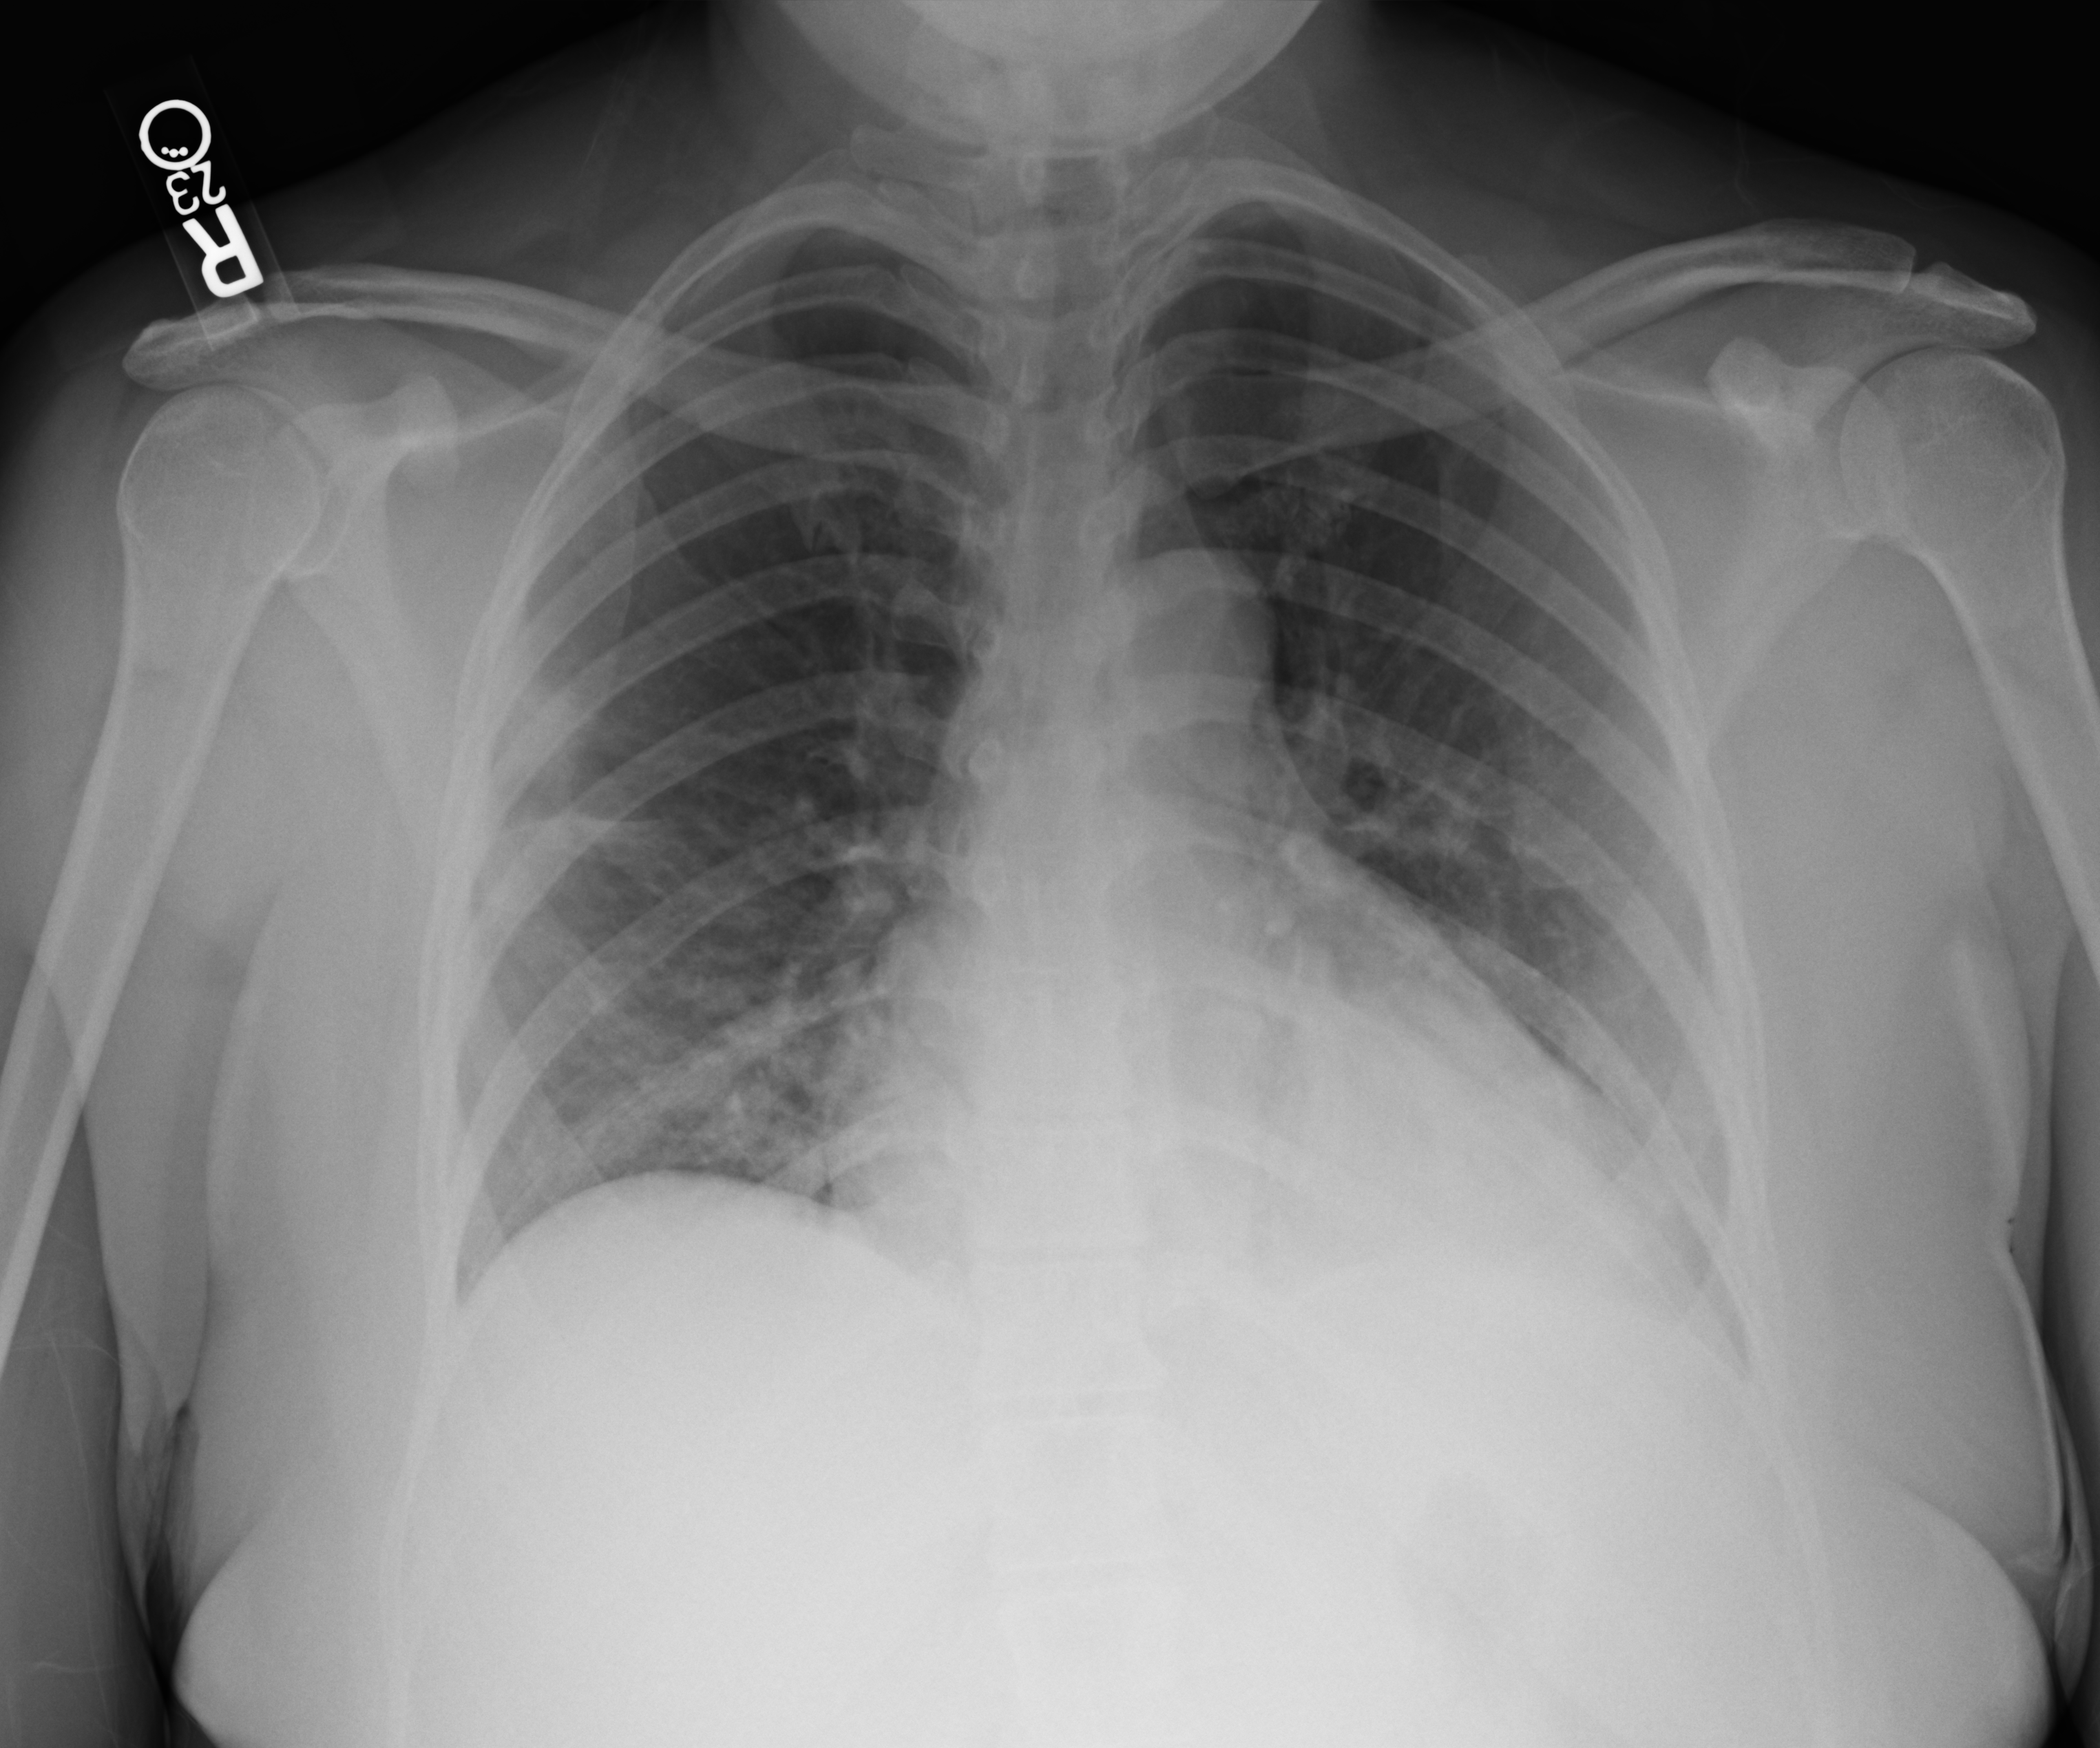
Portable chest radiograph; anteroposterior (AP) projection. Female patient hospitalised with COVID-19, age 18–59 years.
Hospital-stay facts (about this admission, not read from this image; timing relative to this image not recorded): admitted to intensive care during this hospital stay: no.